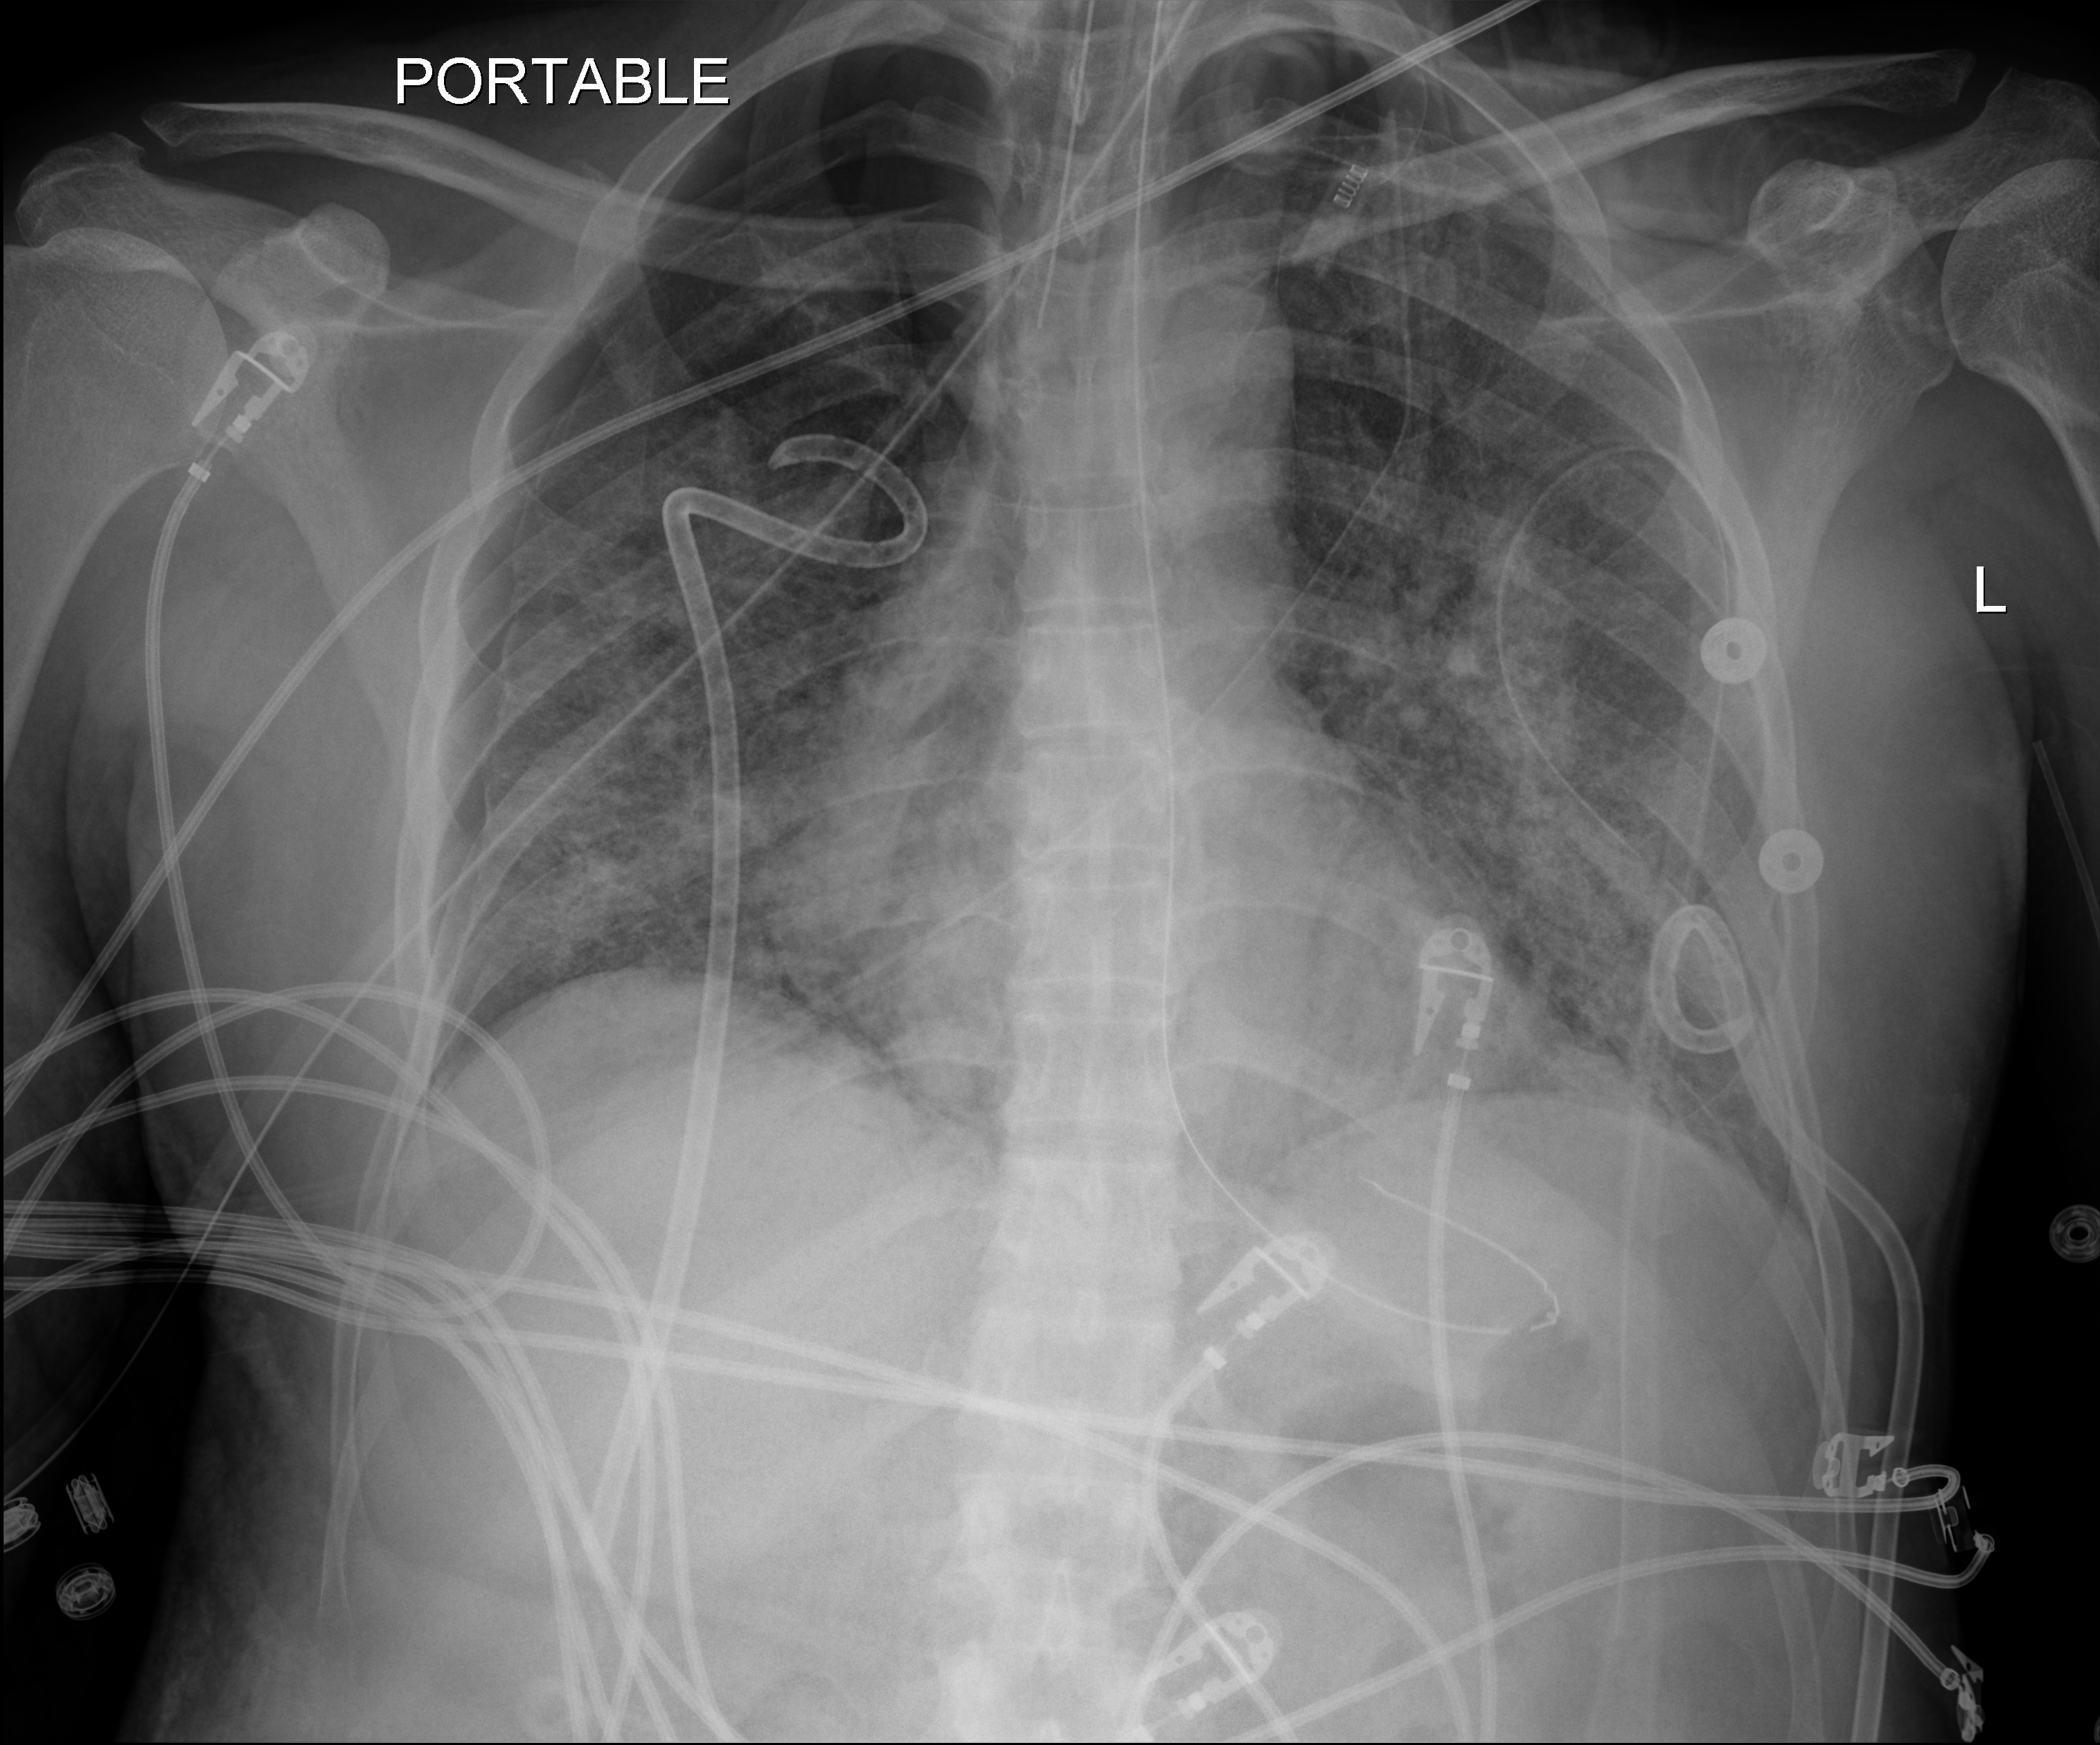
Chest X-ray (portable); anteroposterior (AP) projection. Patient hospitalised with COVID-19, aged 18–59 years.
From the hospital-stay record, not from the radiograph (when in the stay this image was taken is not recorded):
- admitted to intensive care during this hospital stay: yes